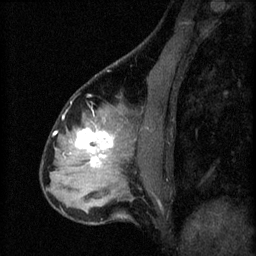
Breast MRI (dynamic contrast-enhanced), one sagittal slice; slice 23 of 60 in the series (ordered by position); 3 images stored at this slice position (order not interpretable as contrast timing); 1.5 T; TE 4.2 ms, TR 8.2 ms; 256 × 256 image matrix, field of view 180 × 180 mm. Patient: female, 37 years.
Outlined on this slice (semi-automatic segmentation, software-assisted and operator-edited):
- analysis volume of interest (the breast-tissue region the enhancement analysis was run in; not a lesion): bounding box <67,120,122,179> (left, top, right, bottom; pixels)
- tumour enhancement mask (voxels above the 70 % enhancement threshold inside the analysis volume of interest): <75,128,114,167>